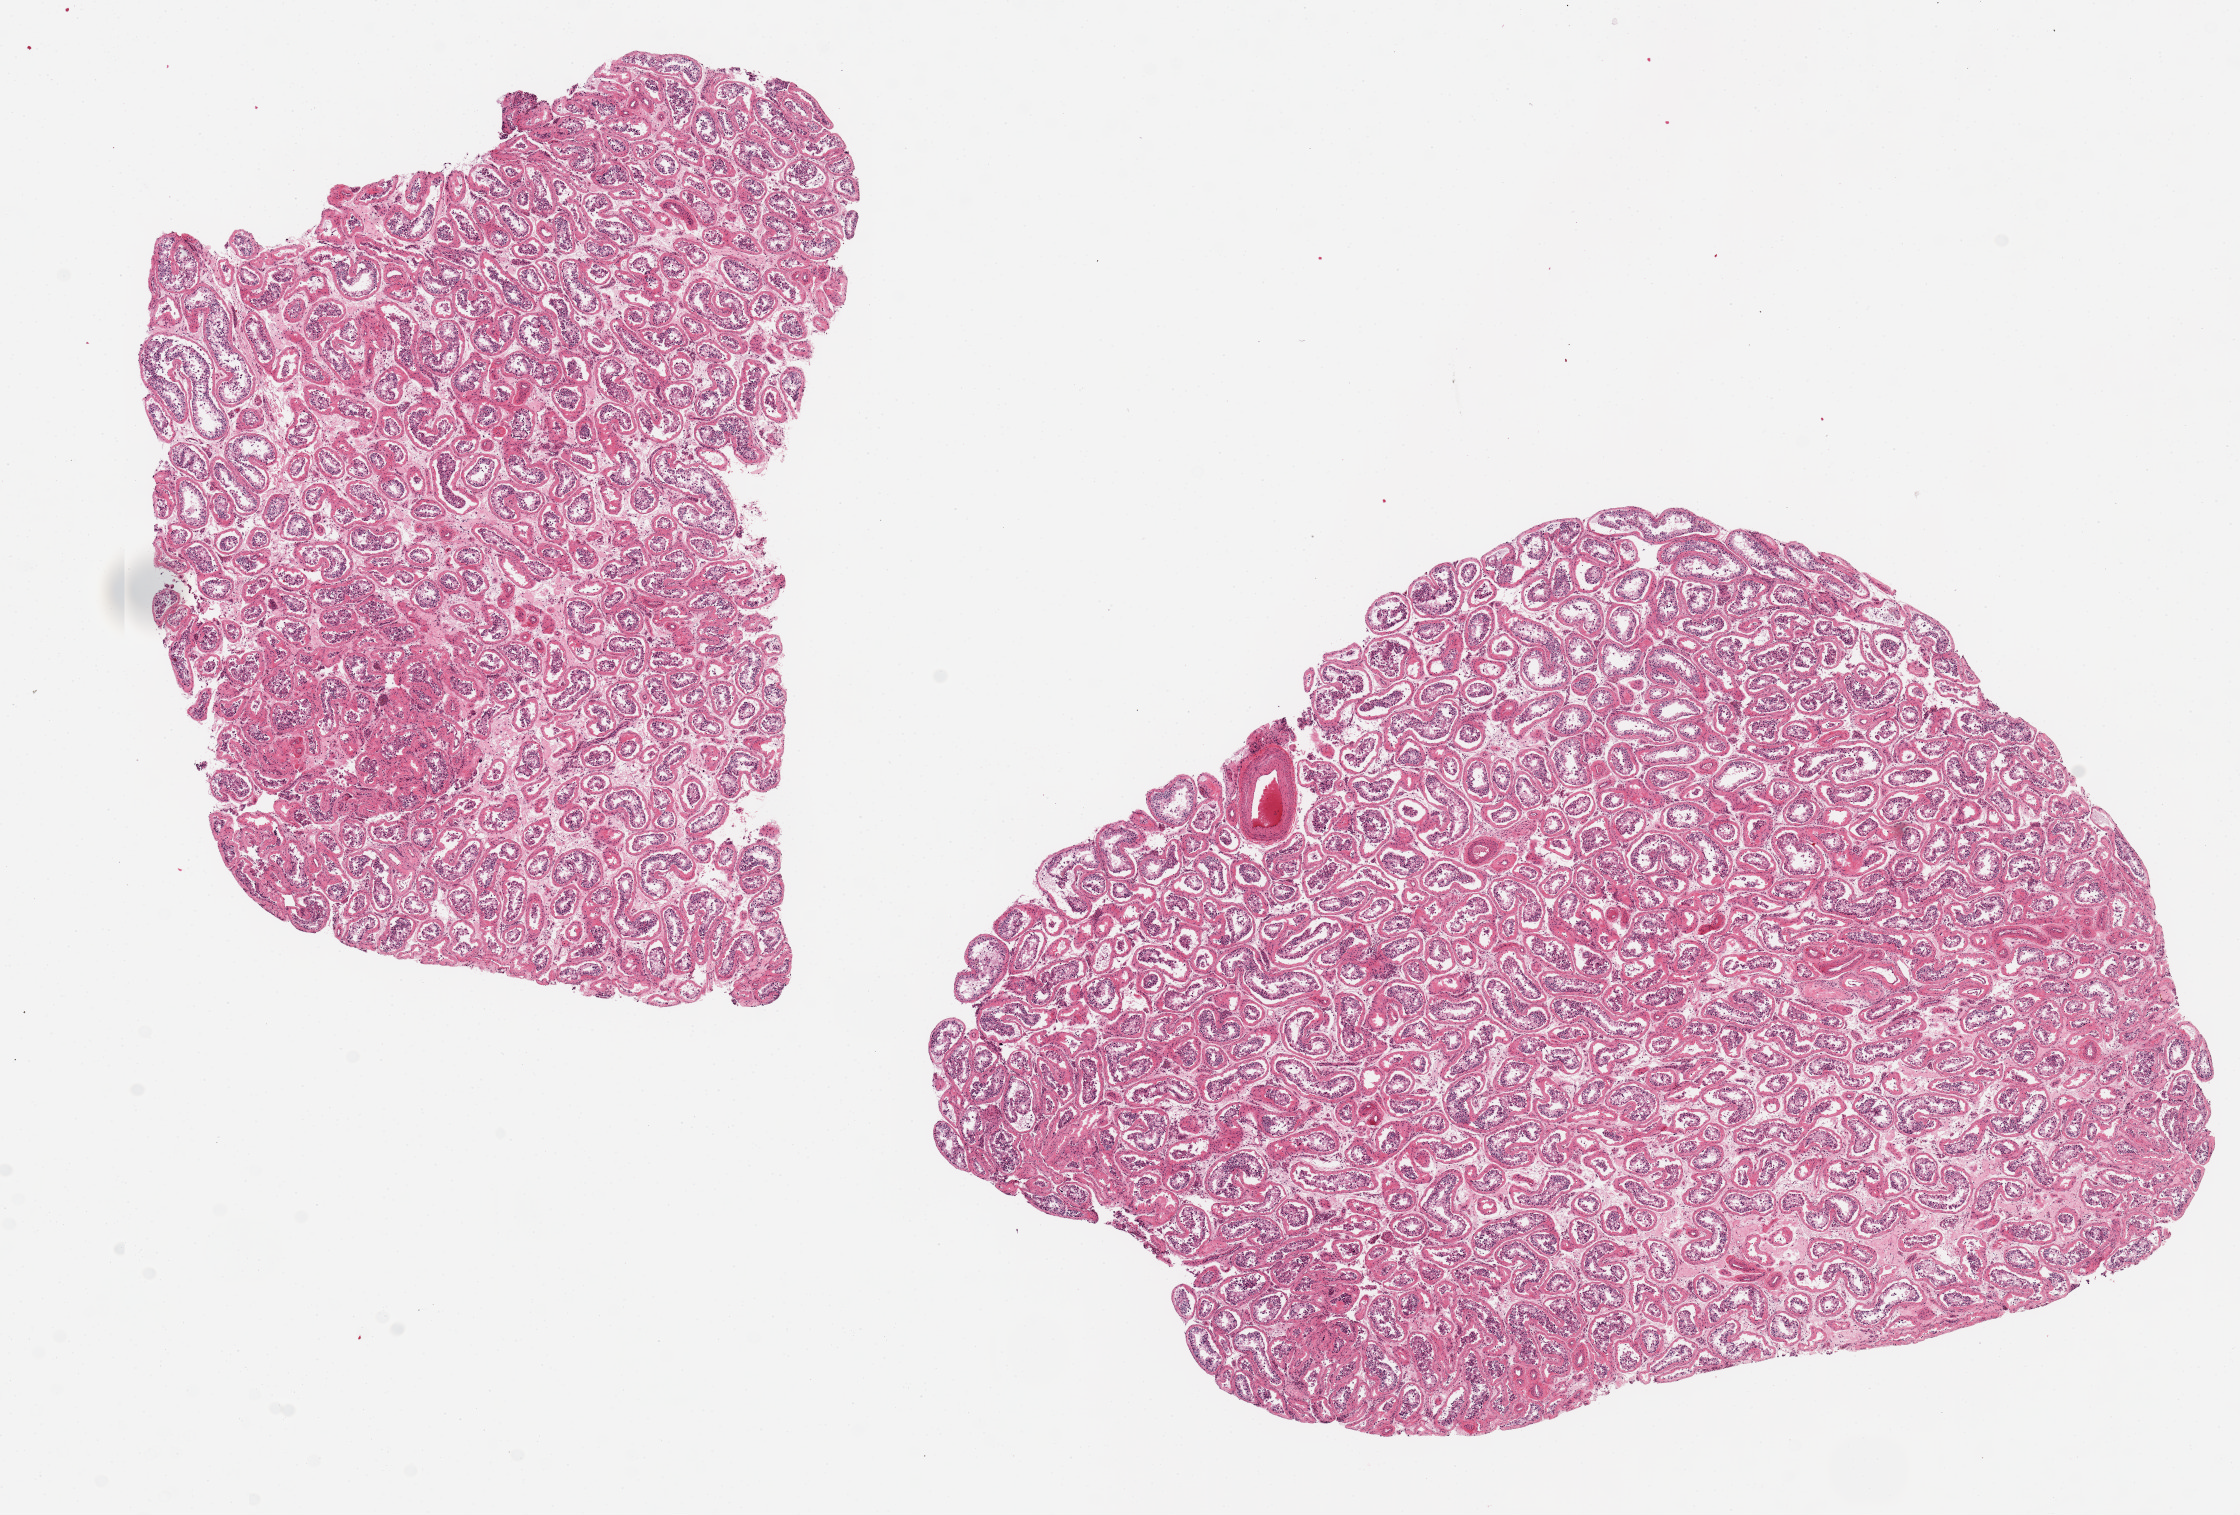
H&E whole-slide image, brightfield, low-resolution overview of the scanned area, about 17.7 x 12.0 mm (from a 20x scan). PAXgene-fixed paraffin-embedded (PFPE) section. Section of testis (target tissue). Tissue donor sample. Male donor.
Reviewer comment on this tissue sample: 2 ~8.5x6mm aliquots. Spermatogenesis diffusely reduced/arrested.